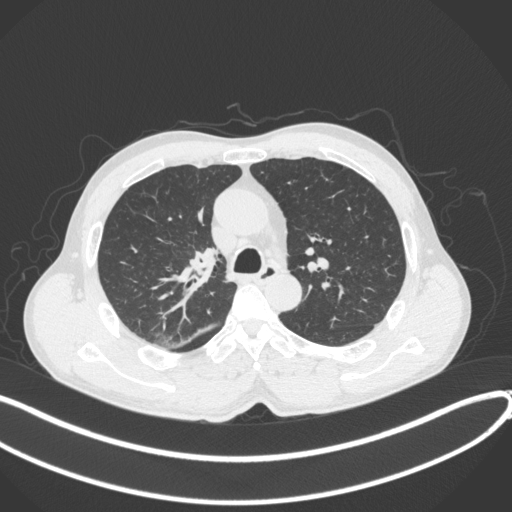
Chest CT, one axial slice. Position 265 of 409 along the scan axis. Reconstruction kernel B31f. 120 kVp. Lung window (W 1500 / L -600 HU). 1 mm slice thickness. 512 × 512 image matrix, field of view 400 × 400 mm. Male patient, age 53 years. From the clinical record (not read from this slice): clinical TNM (as recorded): T1b N0 M0.
Outlined on this slice (rectangle marked by the reading radiologist):
- lung tumour (recorded histology: squamous cell carcinoma): box from (x=187, y=247) to (x=222, y=285) px